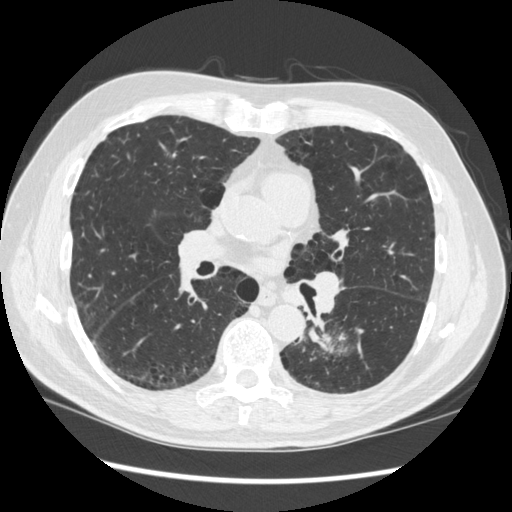
Low-dose screening chest CT, one axial slice; lung window (W 1500 / L -600 HU); 1.25 mm slice thickness; 512 × 512 image matrix, field of view 360 × 360 mm.
Outlined on this slice (manually delineated by an expert):
- lesion 1 (tumor, lower lobe of left lung): bounding box <322,341,346,357> (left, top, right, bottom; pixels)